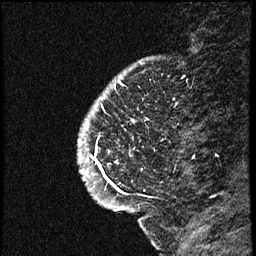
Breast MRI (dynamic contrast-enhanced), one sagittal slice; position 11 of 66 along the scan axis; dynamic contrast-enhanced study with each time point stored as its own series, time point 2 of 3 at this slice position (early post-contrast, ordered by acquisition time); 1.5 T; TE 4.2 ms, TR 17.6 ms; 2 mm slice thickness; 256 × 256 image matrix. Female patient. From the clinical record (not read from this slice): setting: breast cancer imaged before/during neoadjuvant chemotherapy; receptor status: HER2-positive.
Outlined on this slice (semi-automatically segmented with operator editing):
- analysis volume of interest (the breast-tissue region the enhancement analysis was run in; not a lesion): bounding box [x1, y1, x2, y2] px = [80, 69, 177, 209]
- tumour enhancement mask (voxels above the 100 % enhancement threshold inside the analysis volume of interest): [80, 81, 122, 193]